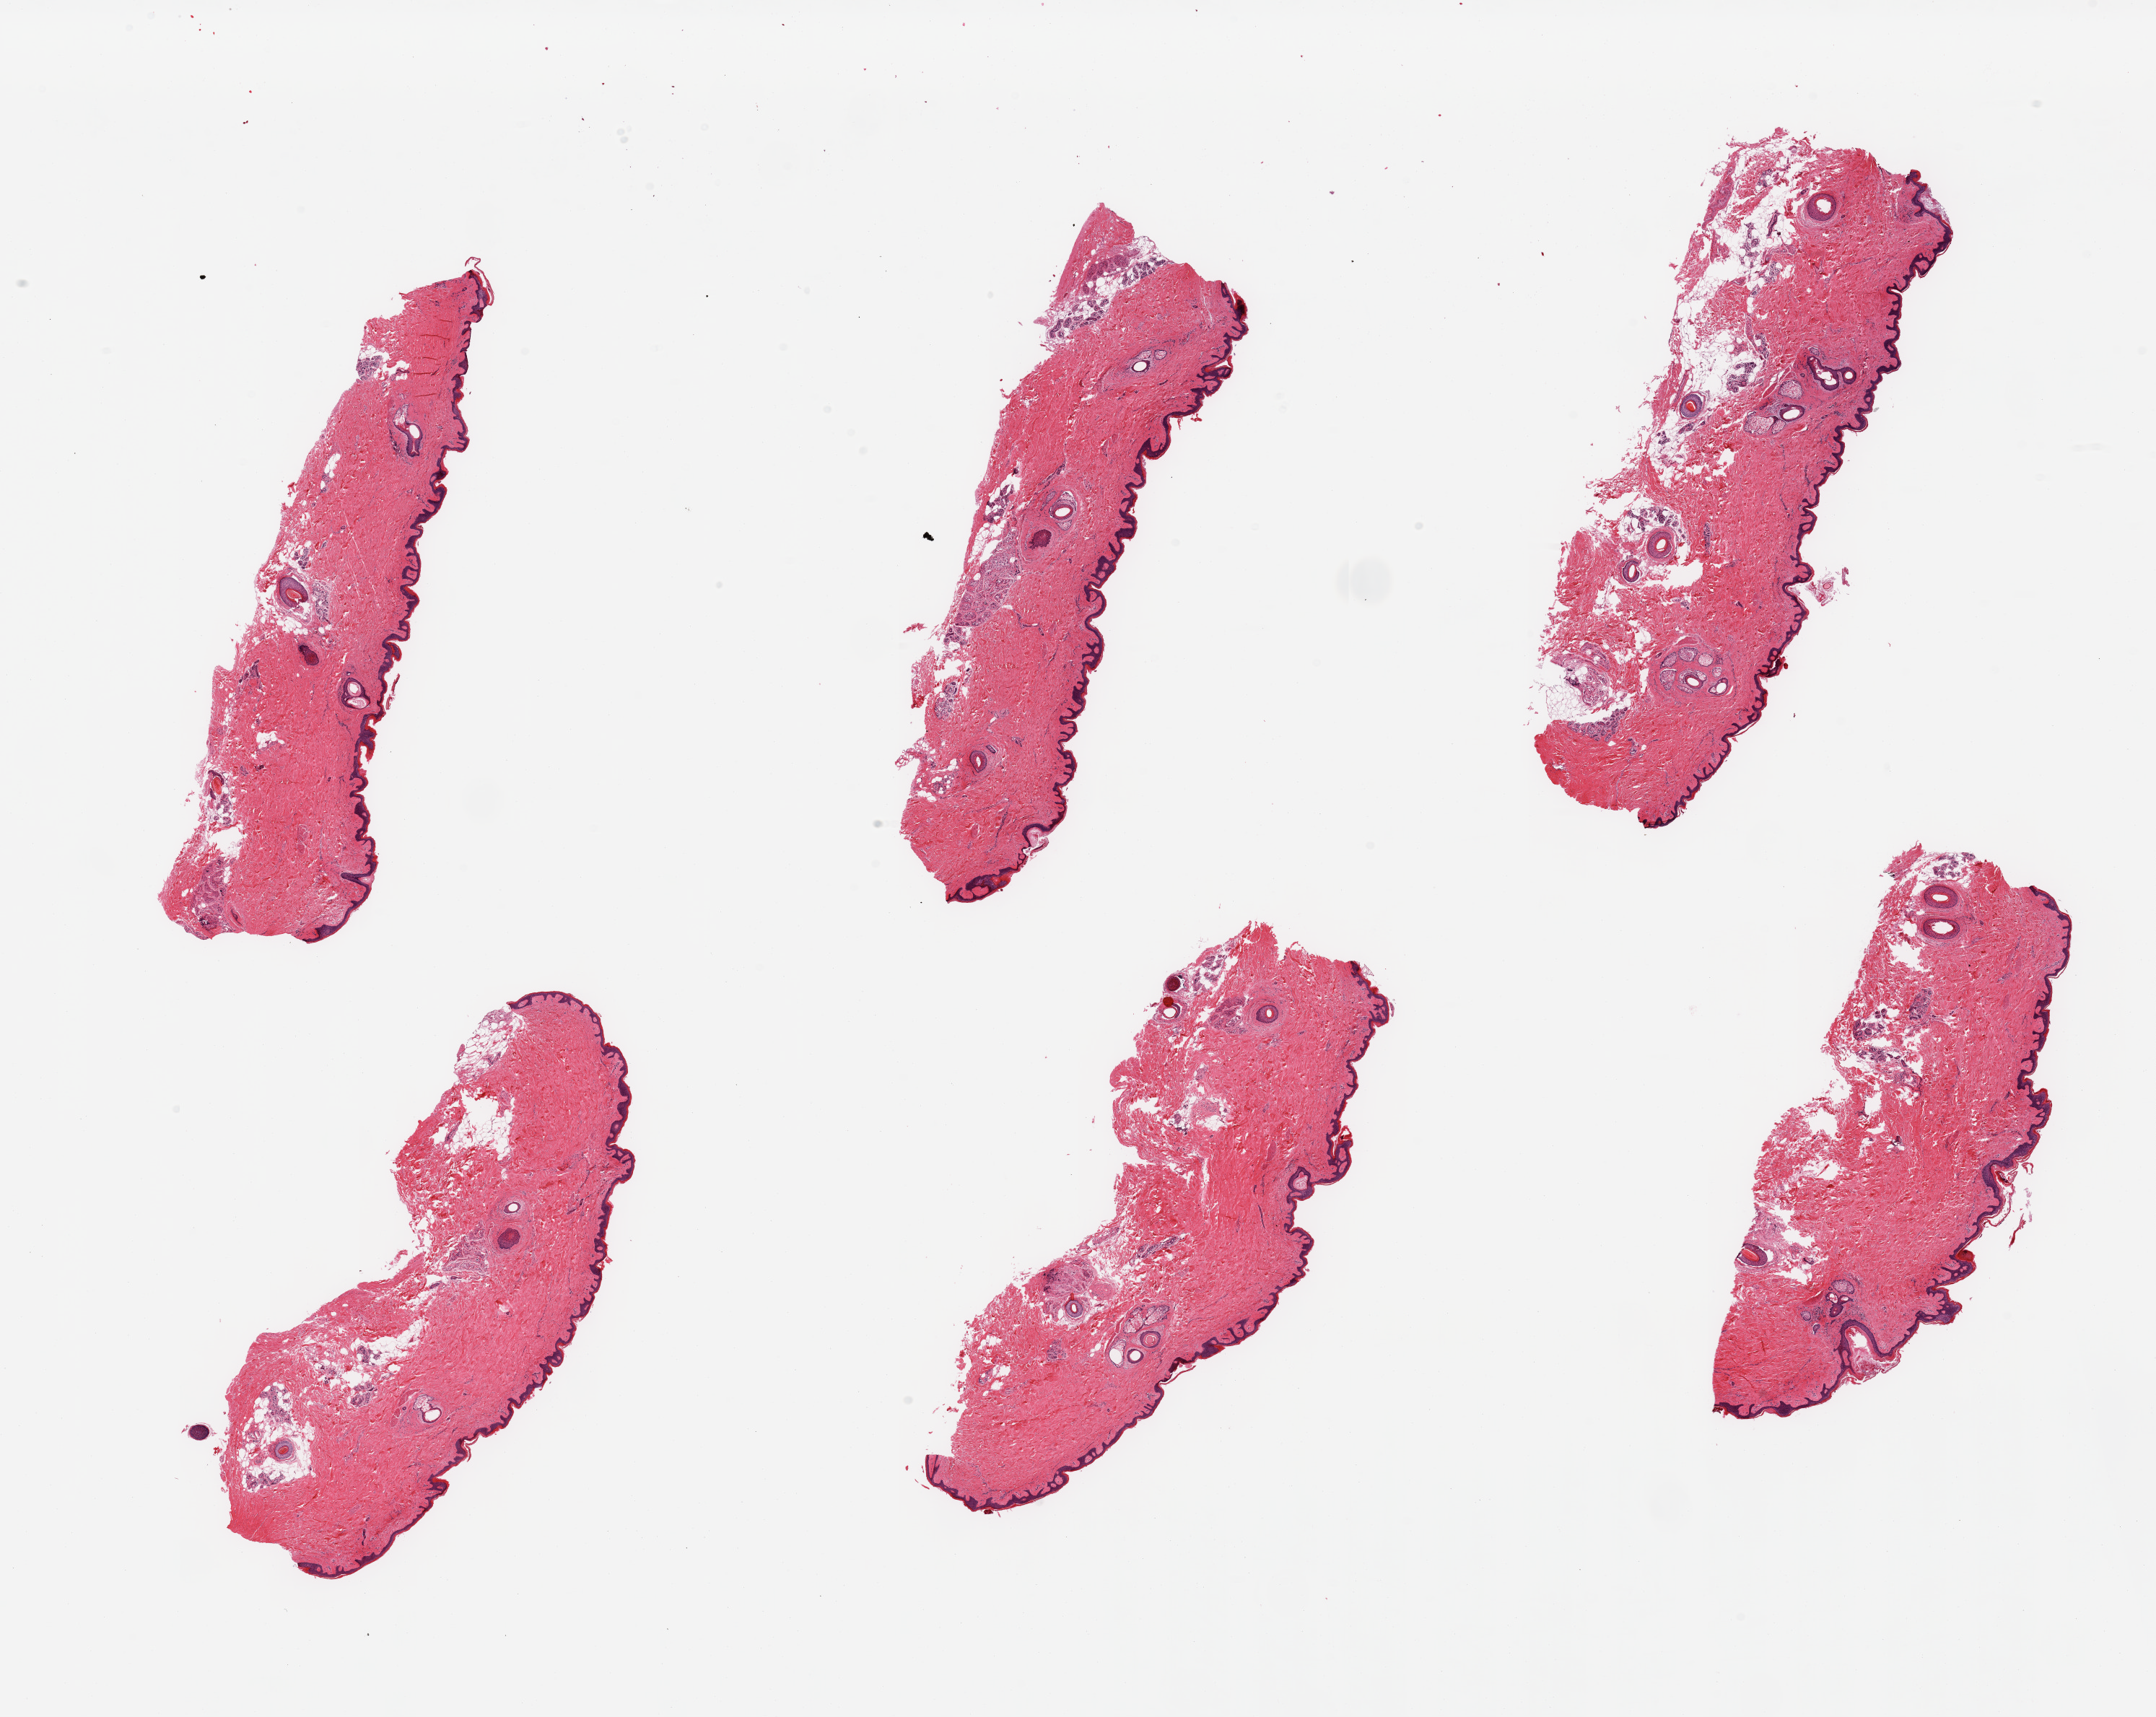
Haematoxylin and eosin whole-slide image, whole scanned area (about 23.6 x 18.8 mm) shown as a low-resolution overview. PAXgene-fixed, paraffin-embedded tissue. Target tissue: skin of suprapubic region. Donor tissue sample. Donor sex: female.
Pathologist's review note for this sample: 6 pieces; well trimmed; 10% dermal fat.